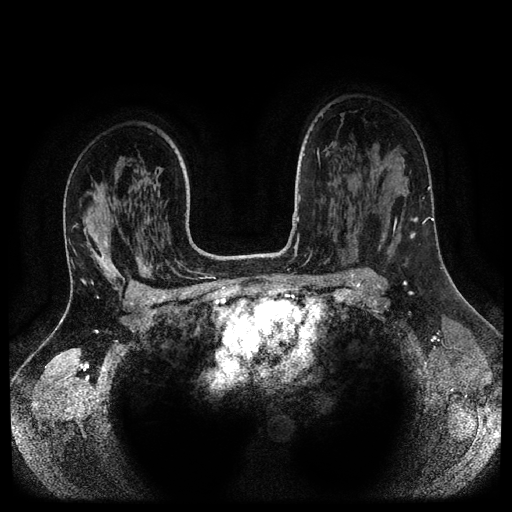
Breast MRI (dynamic contrast-enhanced, multi-phase), one axial slice; slice 72 of 116 in the series (ordered by position); dynamic contrast-enhanced series, time point 2 of 5 at this slice position (early post-contrast); 1.5 T; TE 2.6 ms, TR 5.3 ms; 512 × 512 image matrix. Female patient, age 37 years.
Structures marked on this image (semi-automatic segmentation, software-assisted and operator-edited):
- breast lesion (labelled 'tumour' in the annotation; benign lesions carry a separate 'benign' label): bounding box (x1, y1, x2, y2) in pixels: (410, 217, 418, 239)